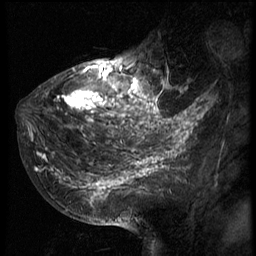
Breast MRI (dynamic contrast-enhanced), one sagittal slice. Slice 25 of 66 in the series (ordered by position). 3 images stored at this slice position (order not interpretable as contrast timing). 1.5 T. TE 4.2 ms, TR 8.9 ms. 256 × 256 image matrix. Female patient, age 39 years. Case-level facts recorded for this patient, not image findings: setting: breast cancer imaged before/during neoadjuvant chemotherapy; receptor status: HER2-positive.
Structures marked on this image (semi-automatic segmentation, software-assisted and operator-edited):
- analysis volume of interest (the breast-tissue region the enhancement analysis was run in; not a lesion): bounding box <29,44,166,196> (left, top, right, bottom; pixels)
- tumour enhancement mask (voxels above the 140 % enhancement threshold inside the analysis volume of interest): <29,62,166,193>